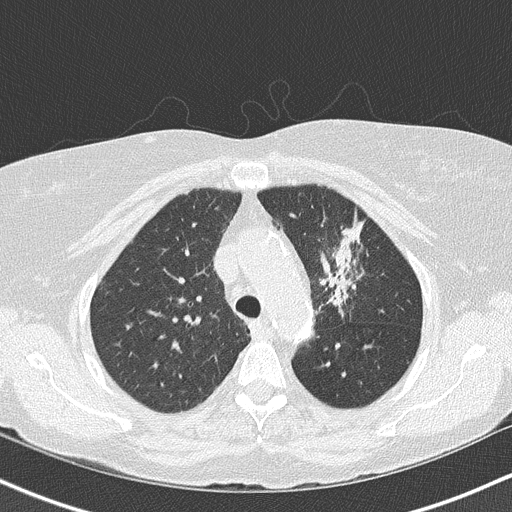
Axial slice from a low-dose chest CT screening exam. Third screening round (two years after baseline). Lung window (W 1500 / L -600 HU). 512 × 512 image matrix, field of view 320 × 320 mm. Female, age 68 years at enrolment. Former smoker at enrolment.
- Expert reader's lesion annotation, bounding box <301,210,383,319> (left, top, right, bottom; pixels).
- The exam's reader record, not a measurement of the box and not confirmed to be the same lesion: non-calcified nodule or mass ≥4 mm, left upper lobe, 5 × 5 mm, poorly defined margins, mixed attenuation, pre-existing on the prior screen: yes; interval growth: yes.
- Official screen result: positive, other.
- Participant outcome: lung cancer diagnosed 42 days after this screen — adenocarcinoma, NOS, left upper lobe, poorly differentiated (G3), stage IB (AJCC 6th edition), 50 mm at pathology.